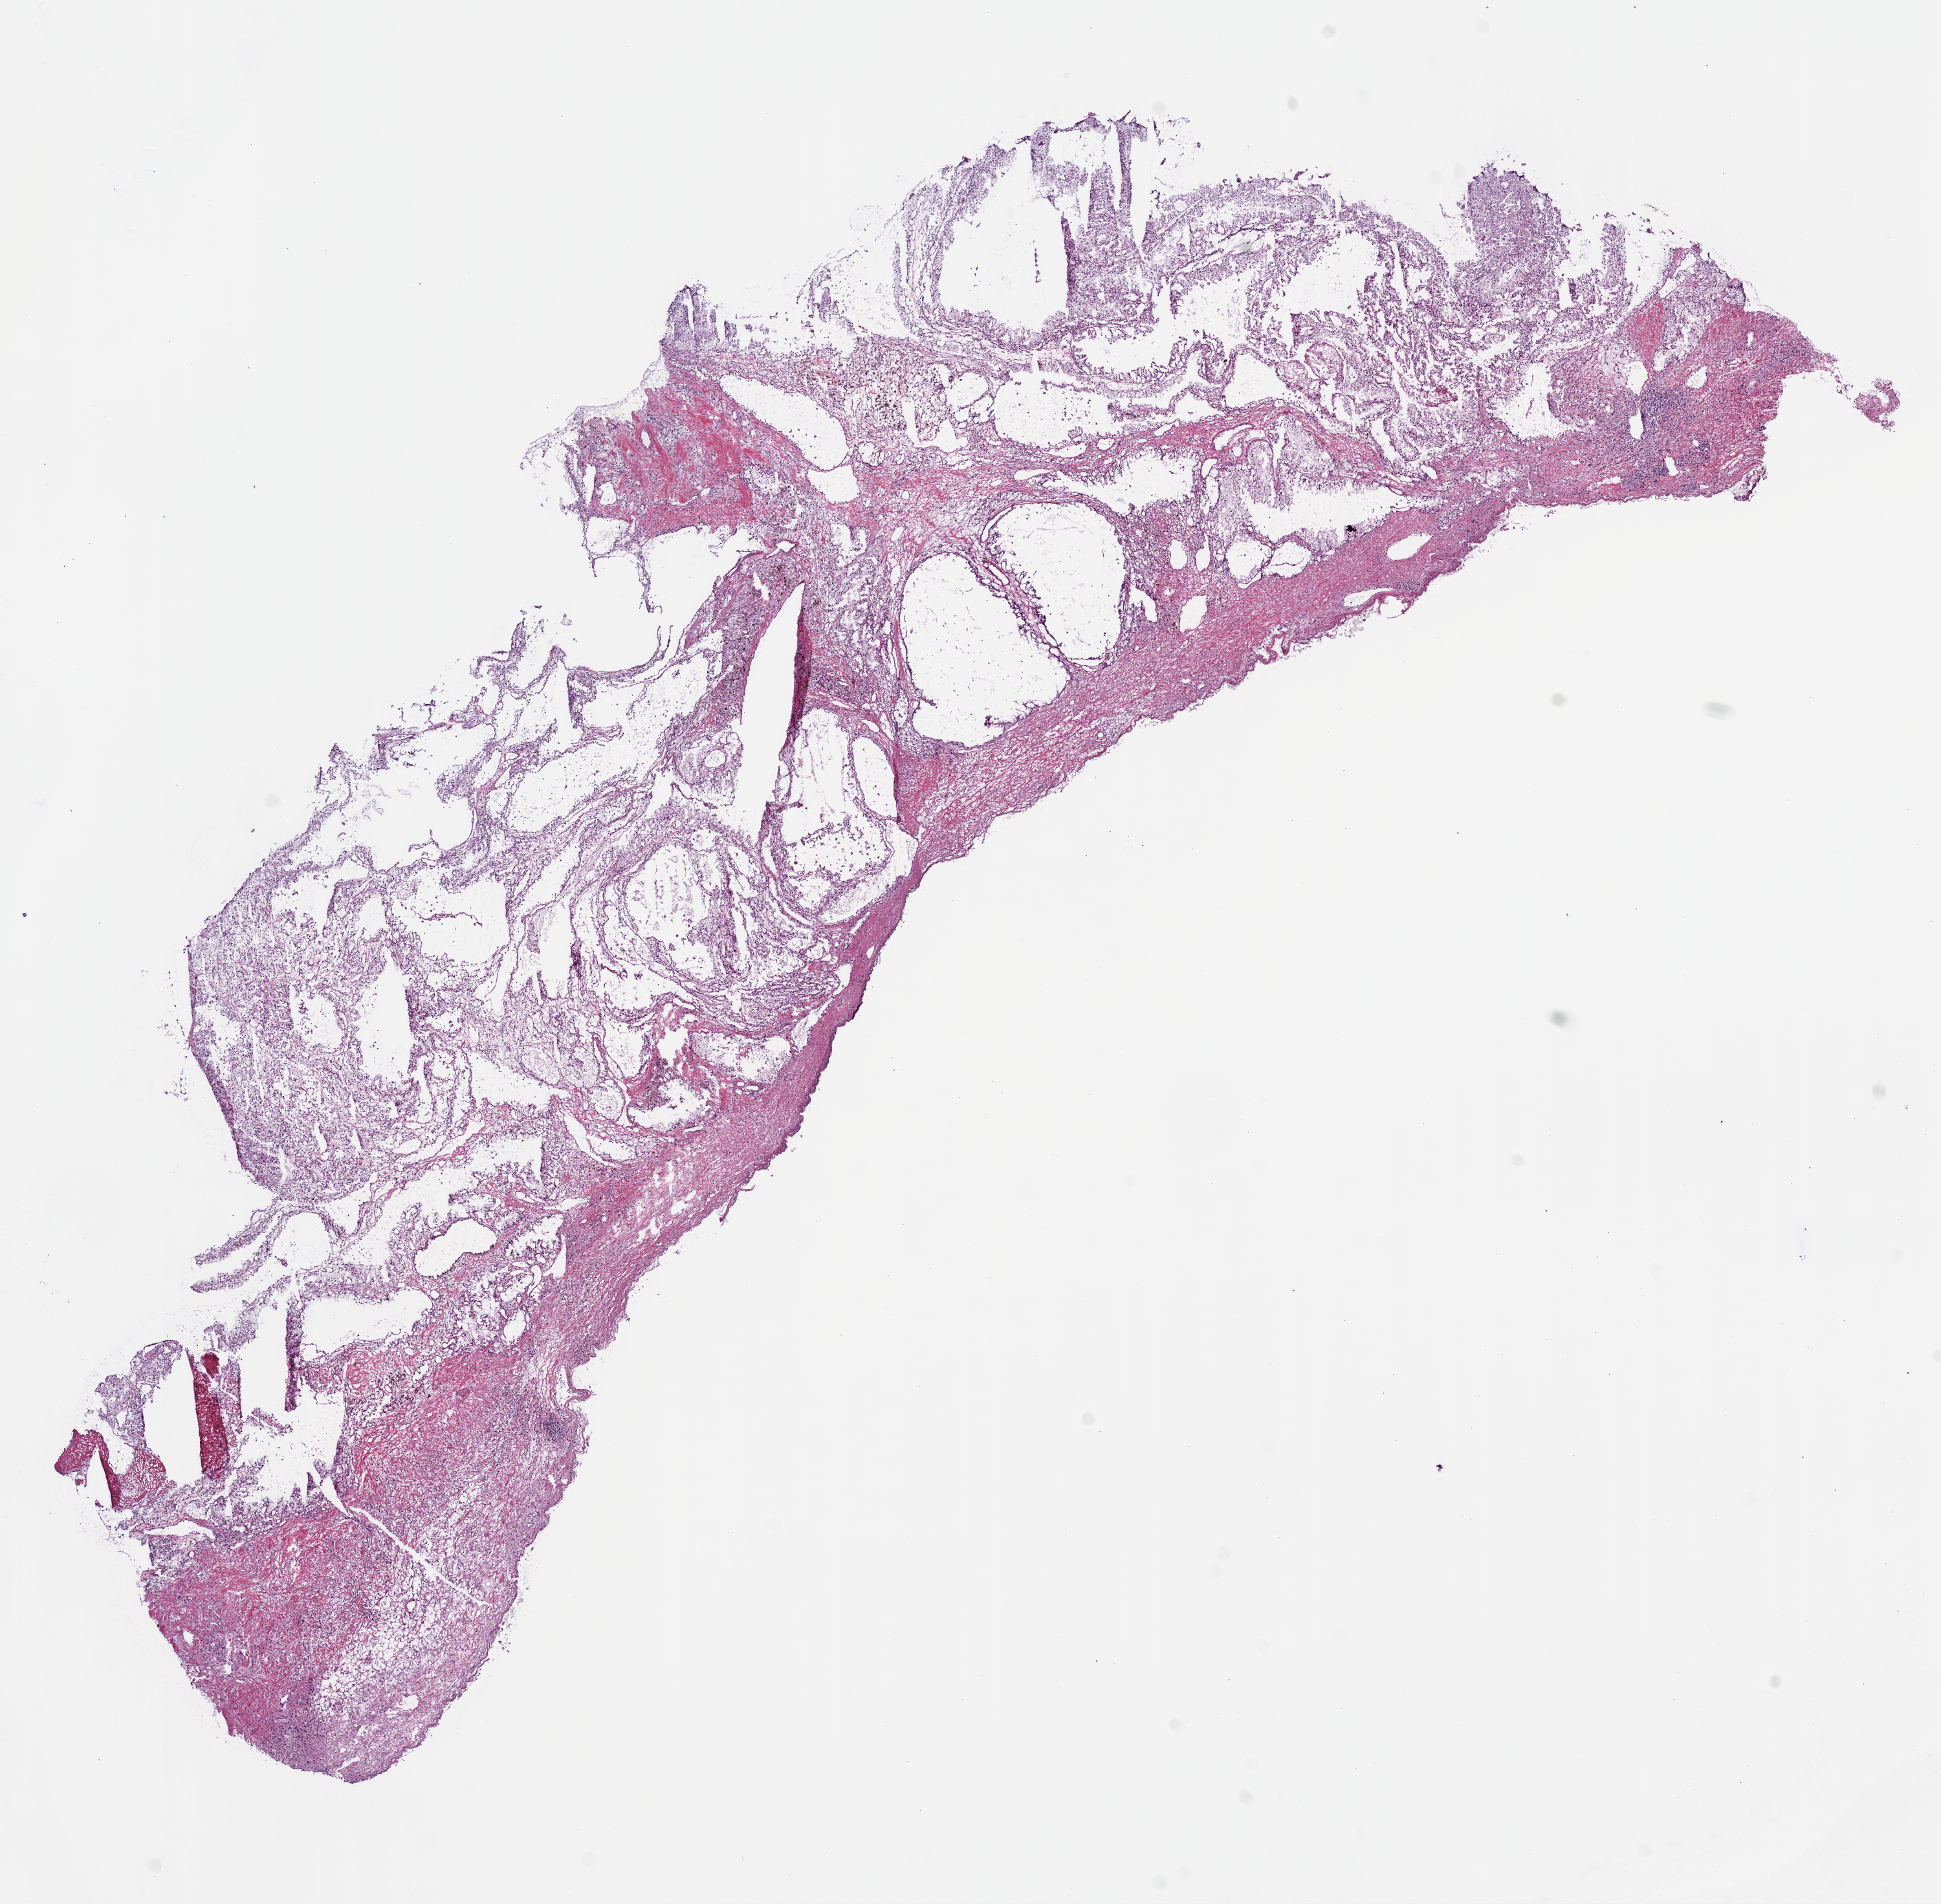
Digitized H&E-stained tissue section (whole slide), low-resolution overview of the scanned area, about 12.0 x 11.8 mm, frozen section from the bottom of the tissue portion, sample: primary tumour, kidney. Patient: male, age at initial diagnosis 56 years. Histologic grade: G3 (poorly differentiated). Slide review estimates, as recorded: tumour cells 80%, tumour nuclei 75%, normal cells 0%, stromal cells 20%, necrosis 0%.
- pathologic diagnosis: Clear cell adenocarcinoma, NOS
- laterality: left
- AJCC pathologic stage: I